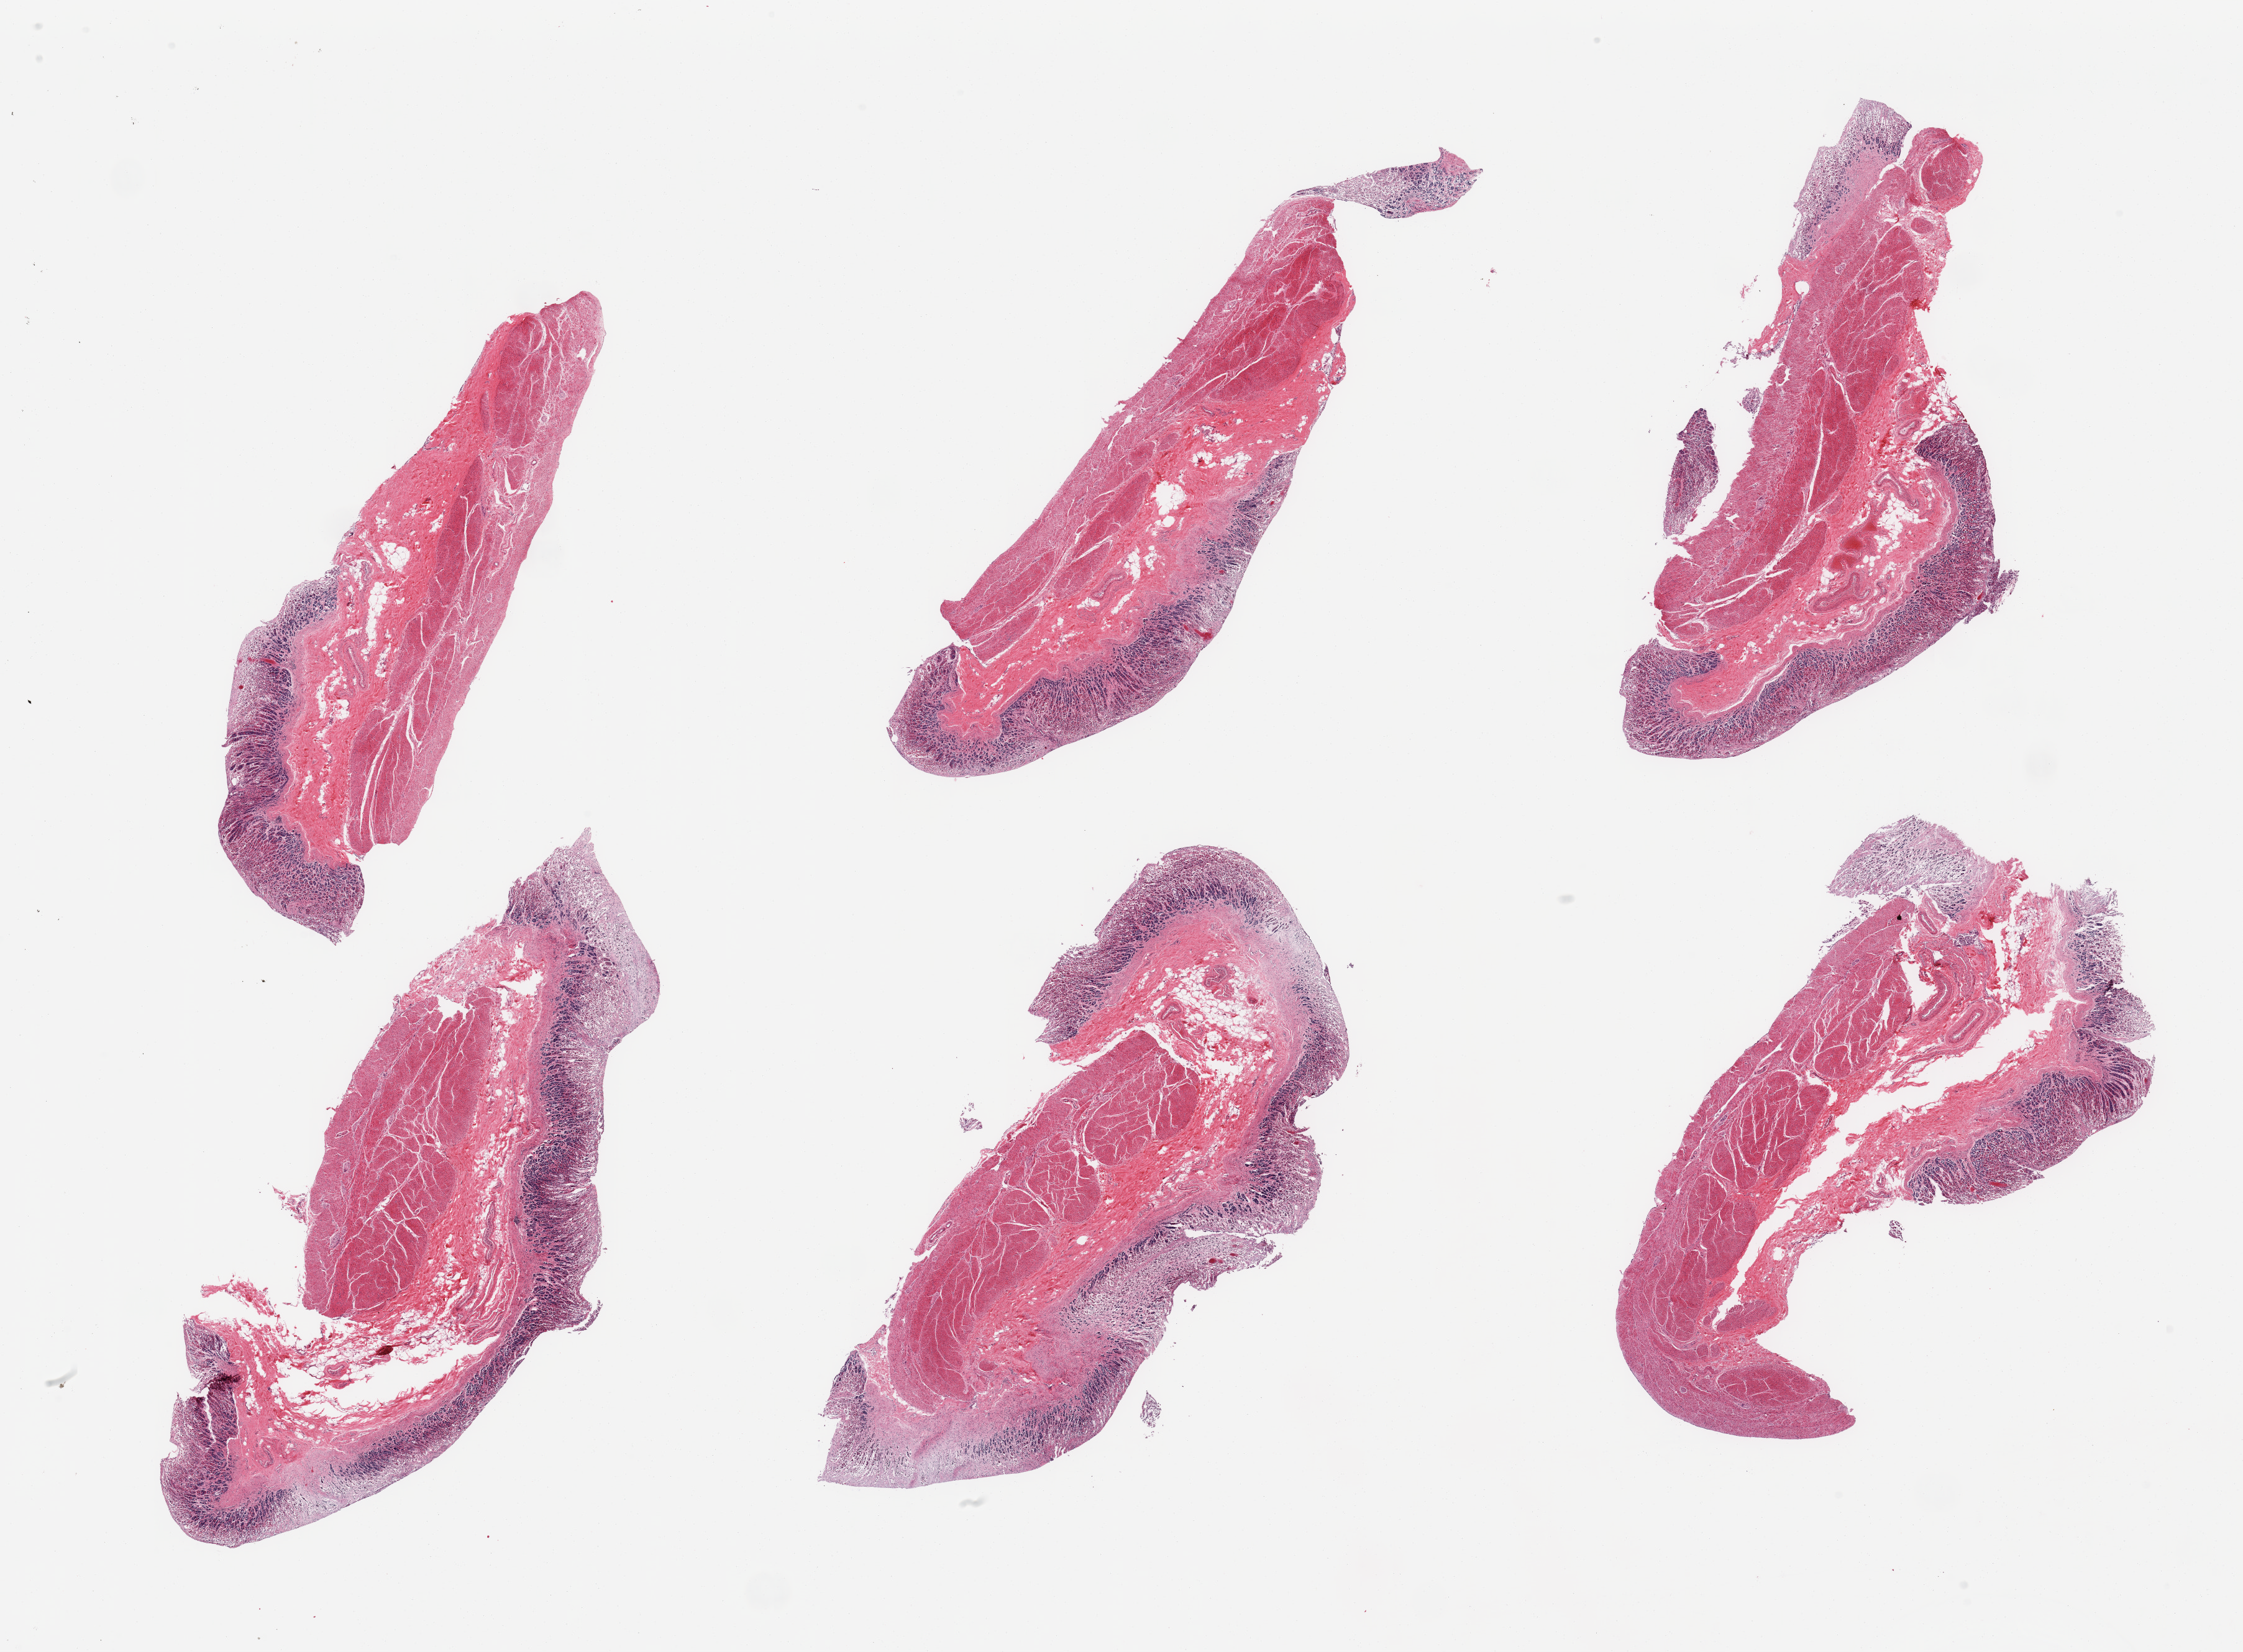
H&E whole-slide image, brightfield — a low-resolution overview of the entire scanned area, about 28.5 x 21.0 mm, PAXgene-fixed paraffin-embedded (PFPE) section, section of stomach (target tissue), tissue donor sample. Female donor.
Pathologist's review note for this sample: 6 pieces; glands in varying states of autolysis.